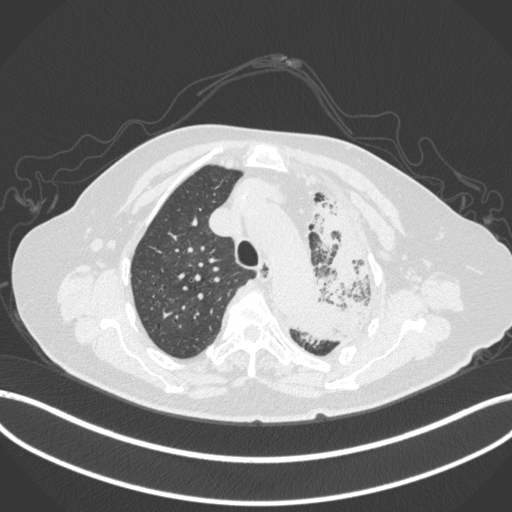
Chest CT, one axial slice. Position 298 of 399 along the scan axis. Reconstruction kernel B31f. 120 kVp. Lung window (W 1500 / L -600 HU). 1 mm slice thickness. 512 × 512 image matrix. Patient: female, 75 years. From the clinical record (not read from this slice): clinical TNM (as recorded): T3 N3 M1.
Outlined on this slice (rectangle marked by the reading radiologist):
- lung tumour (recorded histology: adenocarcinoma): box from (x=283, y=186) to (x=383, y=348) px